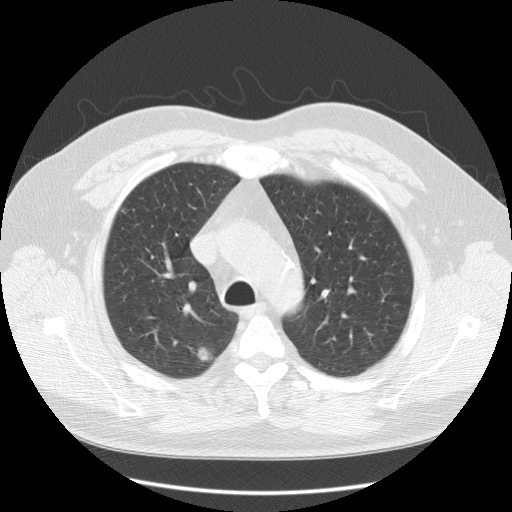
Low-dose screening chest CT, one axial slice. Slice 94 of 125 in the series (ordered by position). Lung window (W 1500 / L -600 HU). 2.5 mm slice thickness. 512 × 512 image matrix, field of view 380 × 380 mm.
Annotated regions visible in this slice (manually delineated by an expert):
- lesion 1 (tumor, upper lobe of right lung): bounding box <197,348,210,361> (left, top, right, bottom; pixels)